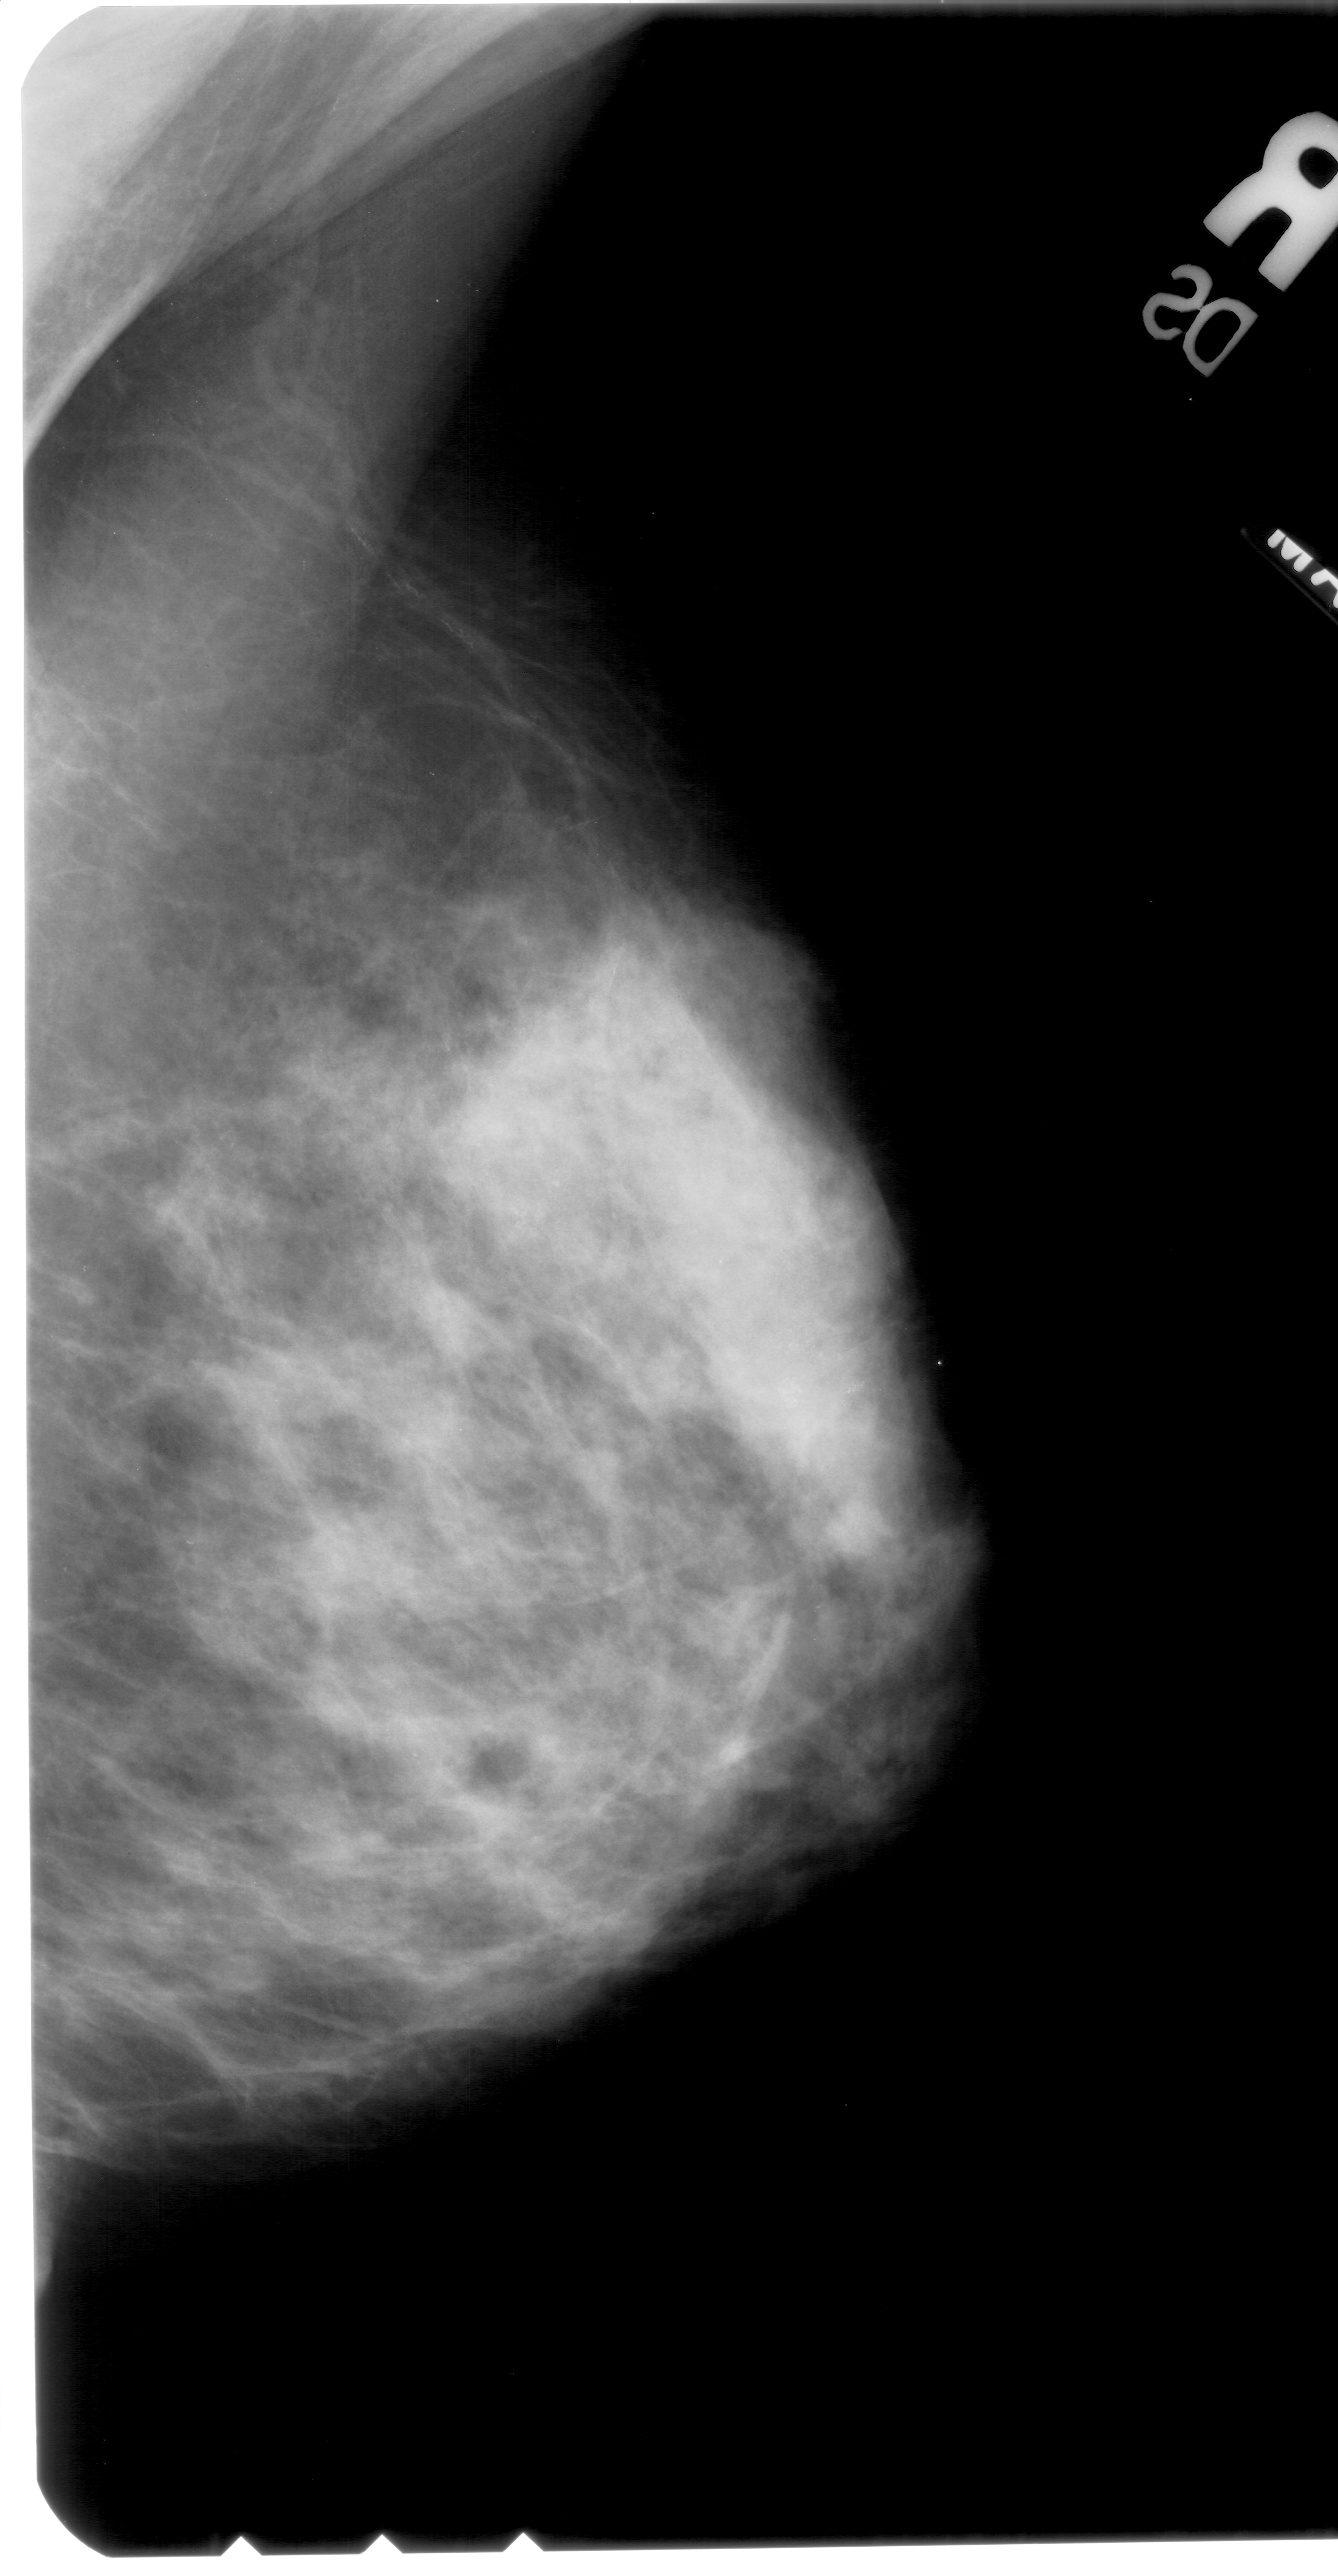
Mammogram (digitized film); right breast; MLO view; 1338 × 2576 image matrix.
Expert-marked regions of interest on this image (one box per marked abnormality):
- calcifications, morphology pleomorphic, distribution segmental; BI-RADS assessment category 4; subtlety rating 1 on a 1 (subtle) to 5 (obvious) scale; pathology result (as recorded, not read from the image): malignant: bounding box (x1, y1, x2, y2) in pixels: (390, 1013, 901, 1437)